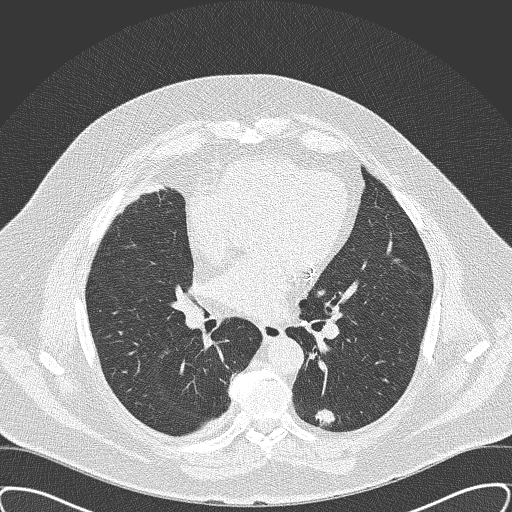
Low-dose screening chest CT, axial slice, third annual screen, lung window (W 1500 / L -600 HU), 2 mm slice thickness, lung (sharp) reconstruction kernel (B50f). Male, age 63 years at enrolment. Former smoker at enrolment.
Expert reader's lesion annotation, box from (x=301, y=392) to (x=353, y=440) px. The screening reader recorded 2 non-calcified nodules or masses ≥4 mm on this exam (left lower lobe, left lower lobe); which of them this box marks is not recorded. Official screen result: positive, other. Lung cancer was diagnosed 47 days after this screen: squamous cell carcinoma, NOS, left lower lobe, moderately differentiated (G2), stage IA (AJCC 6th edition), 15 mm at pathology.